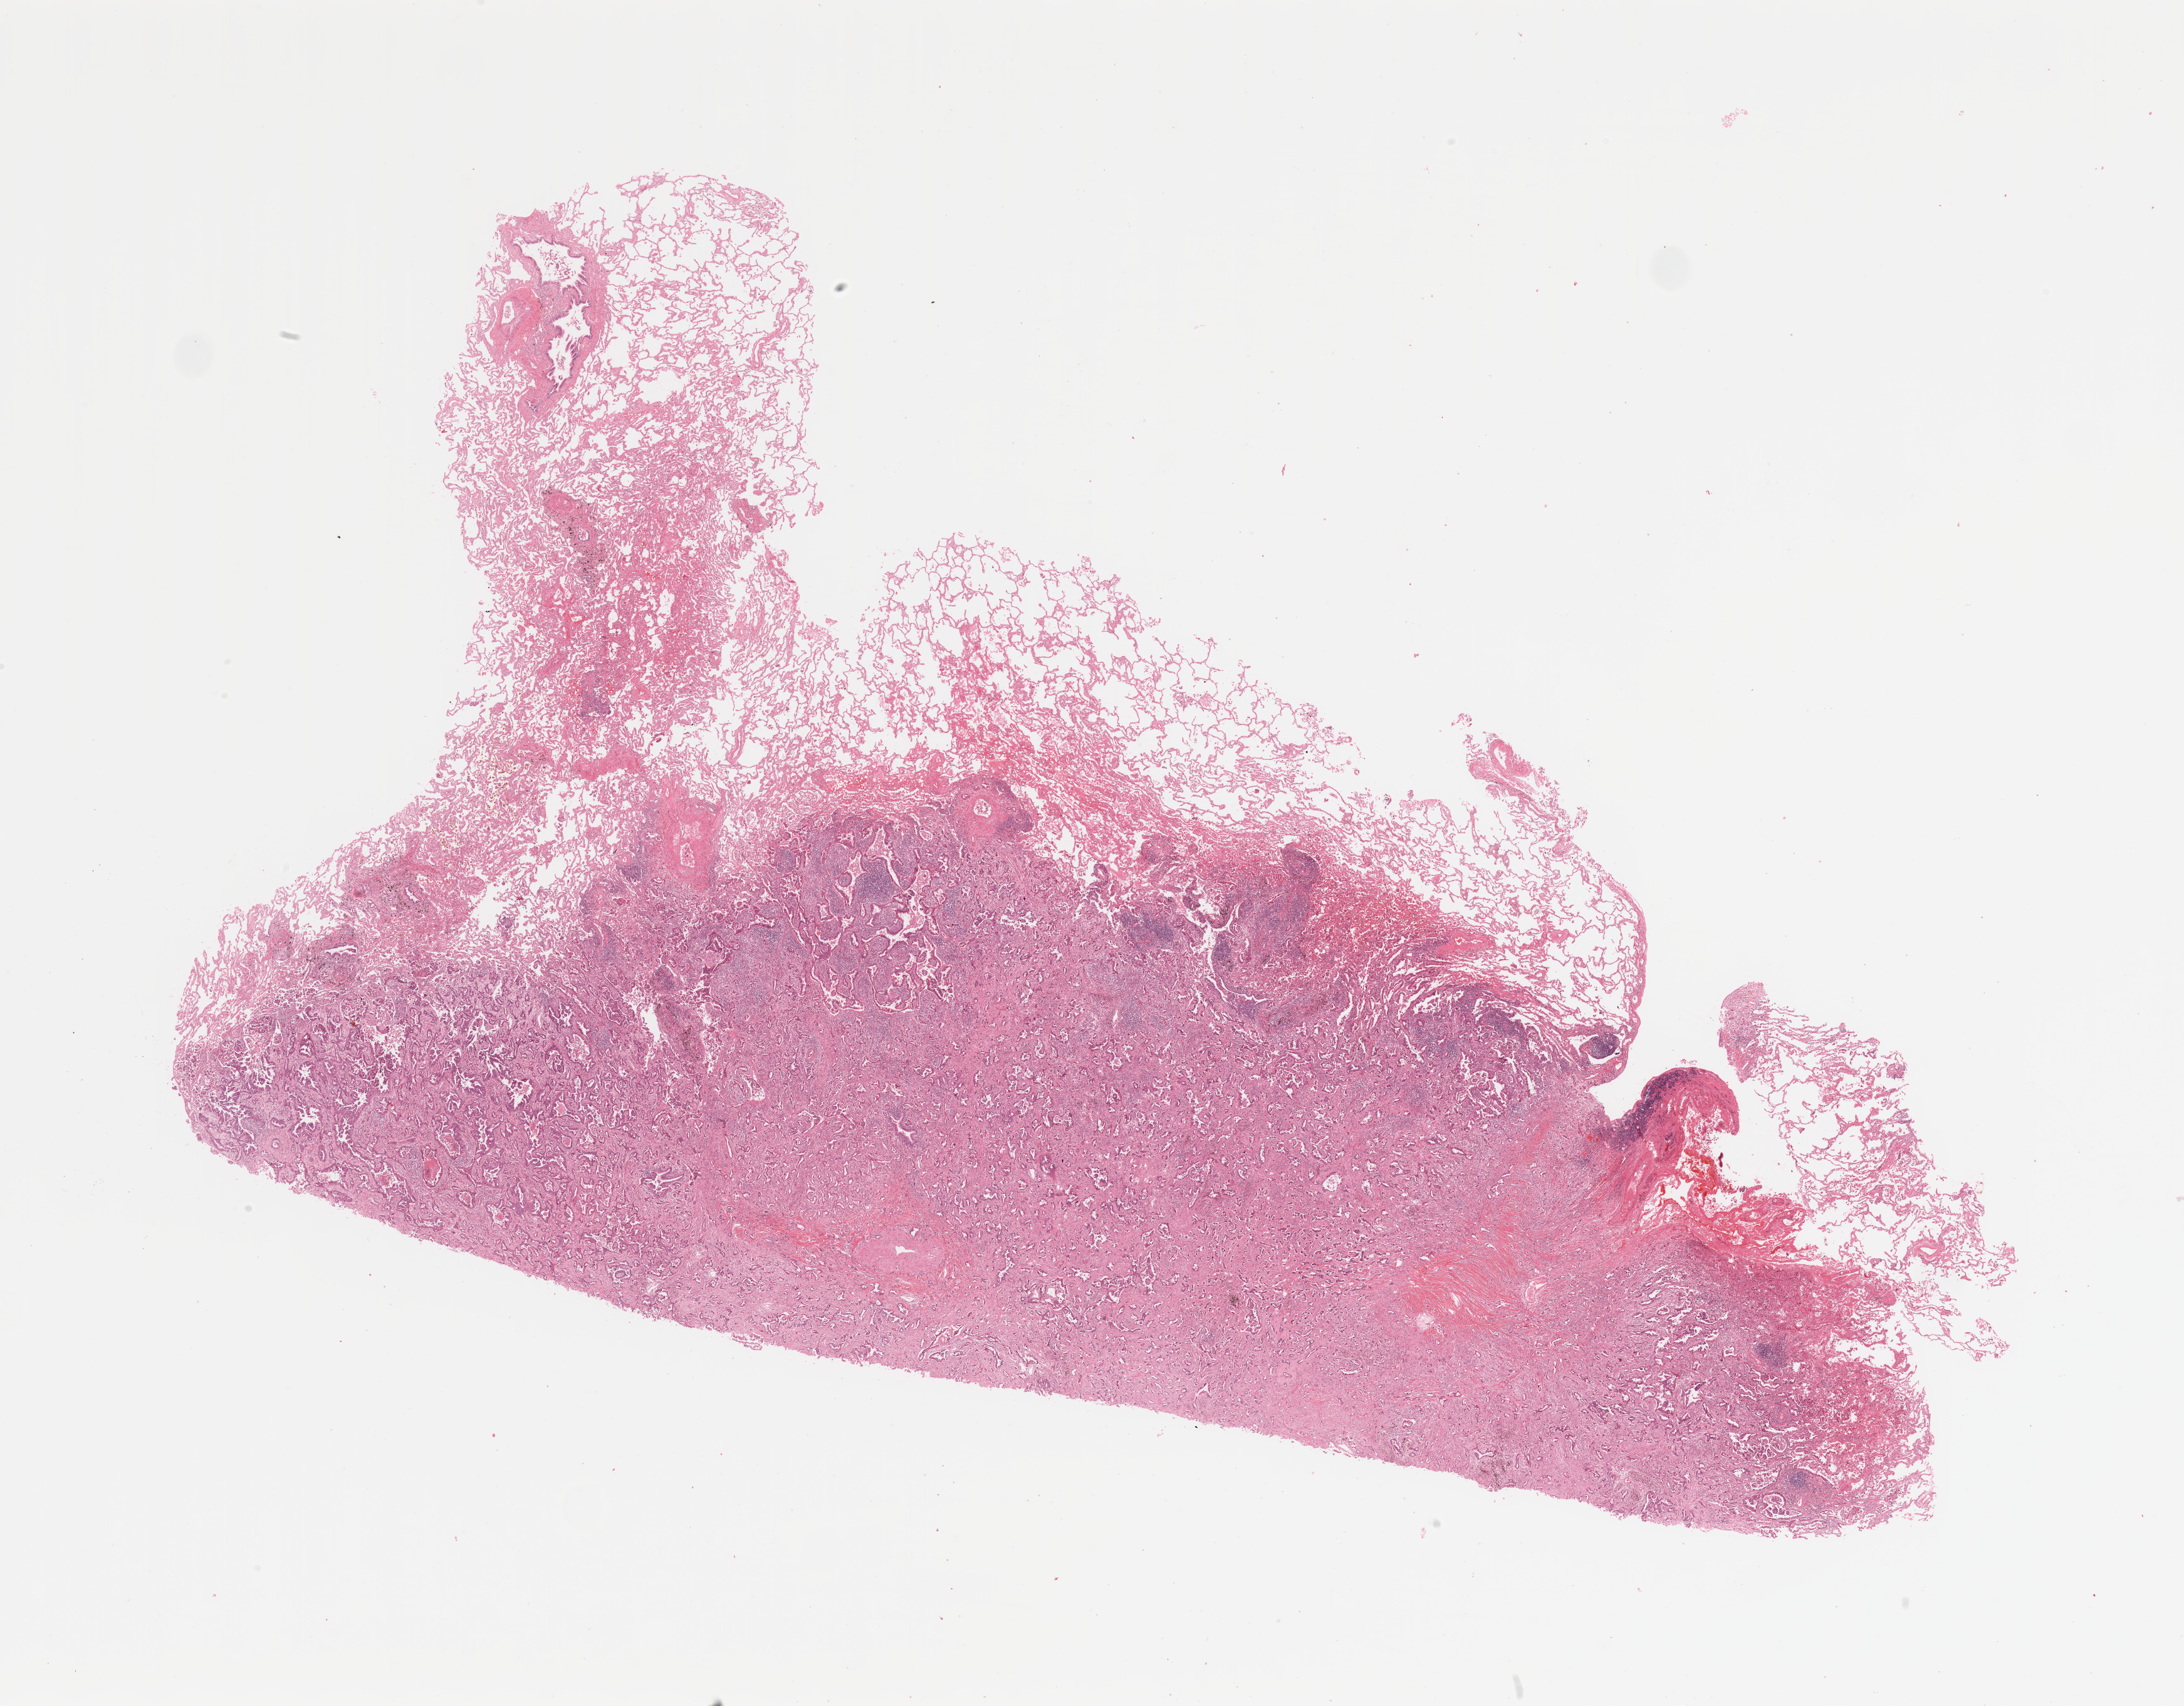
Digitized H&E tissue section (whole slide) — a low-resolution overview of the entire scanned area, about 27.6 x 21.5 mm (from a 20x scan); lung, tumour tissue. 65-year-old female patient. Histologic grade: G3 (poorly differentiated).
• AJCC pathologic stage: IB
• diagnosis: Adenocarcinoma, NOS